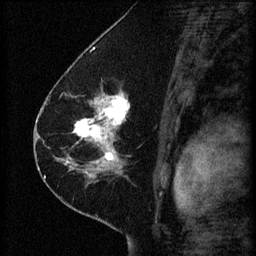
Breast MRI (dynamic contrast-enhanced), one sagittal slice; slice 36 of 60 in the series (ordered by position); 3 images stored at this slice position (order not interpretable as contrast timing); 1.5 T; TE 4.2 ms, TR 8.2 ms; 256 × 256 image matrix, field of view 180 × 180 mm. Patient: female, 41 years.
Outlined on this slice (semi-automatically segmented with operator editing):
- analysis volume of interest (the breast-tissue region the enhancement analysis was run in; not a lesion): bounding box <67,92,165,173> (left, top, right, bottom; pixels)
- tumour enhancement mask (voxels above the 70 % enhancement threshold inside the analysis volume of interest): <67,92,128,173>